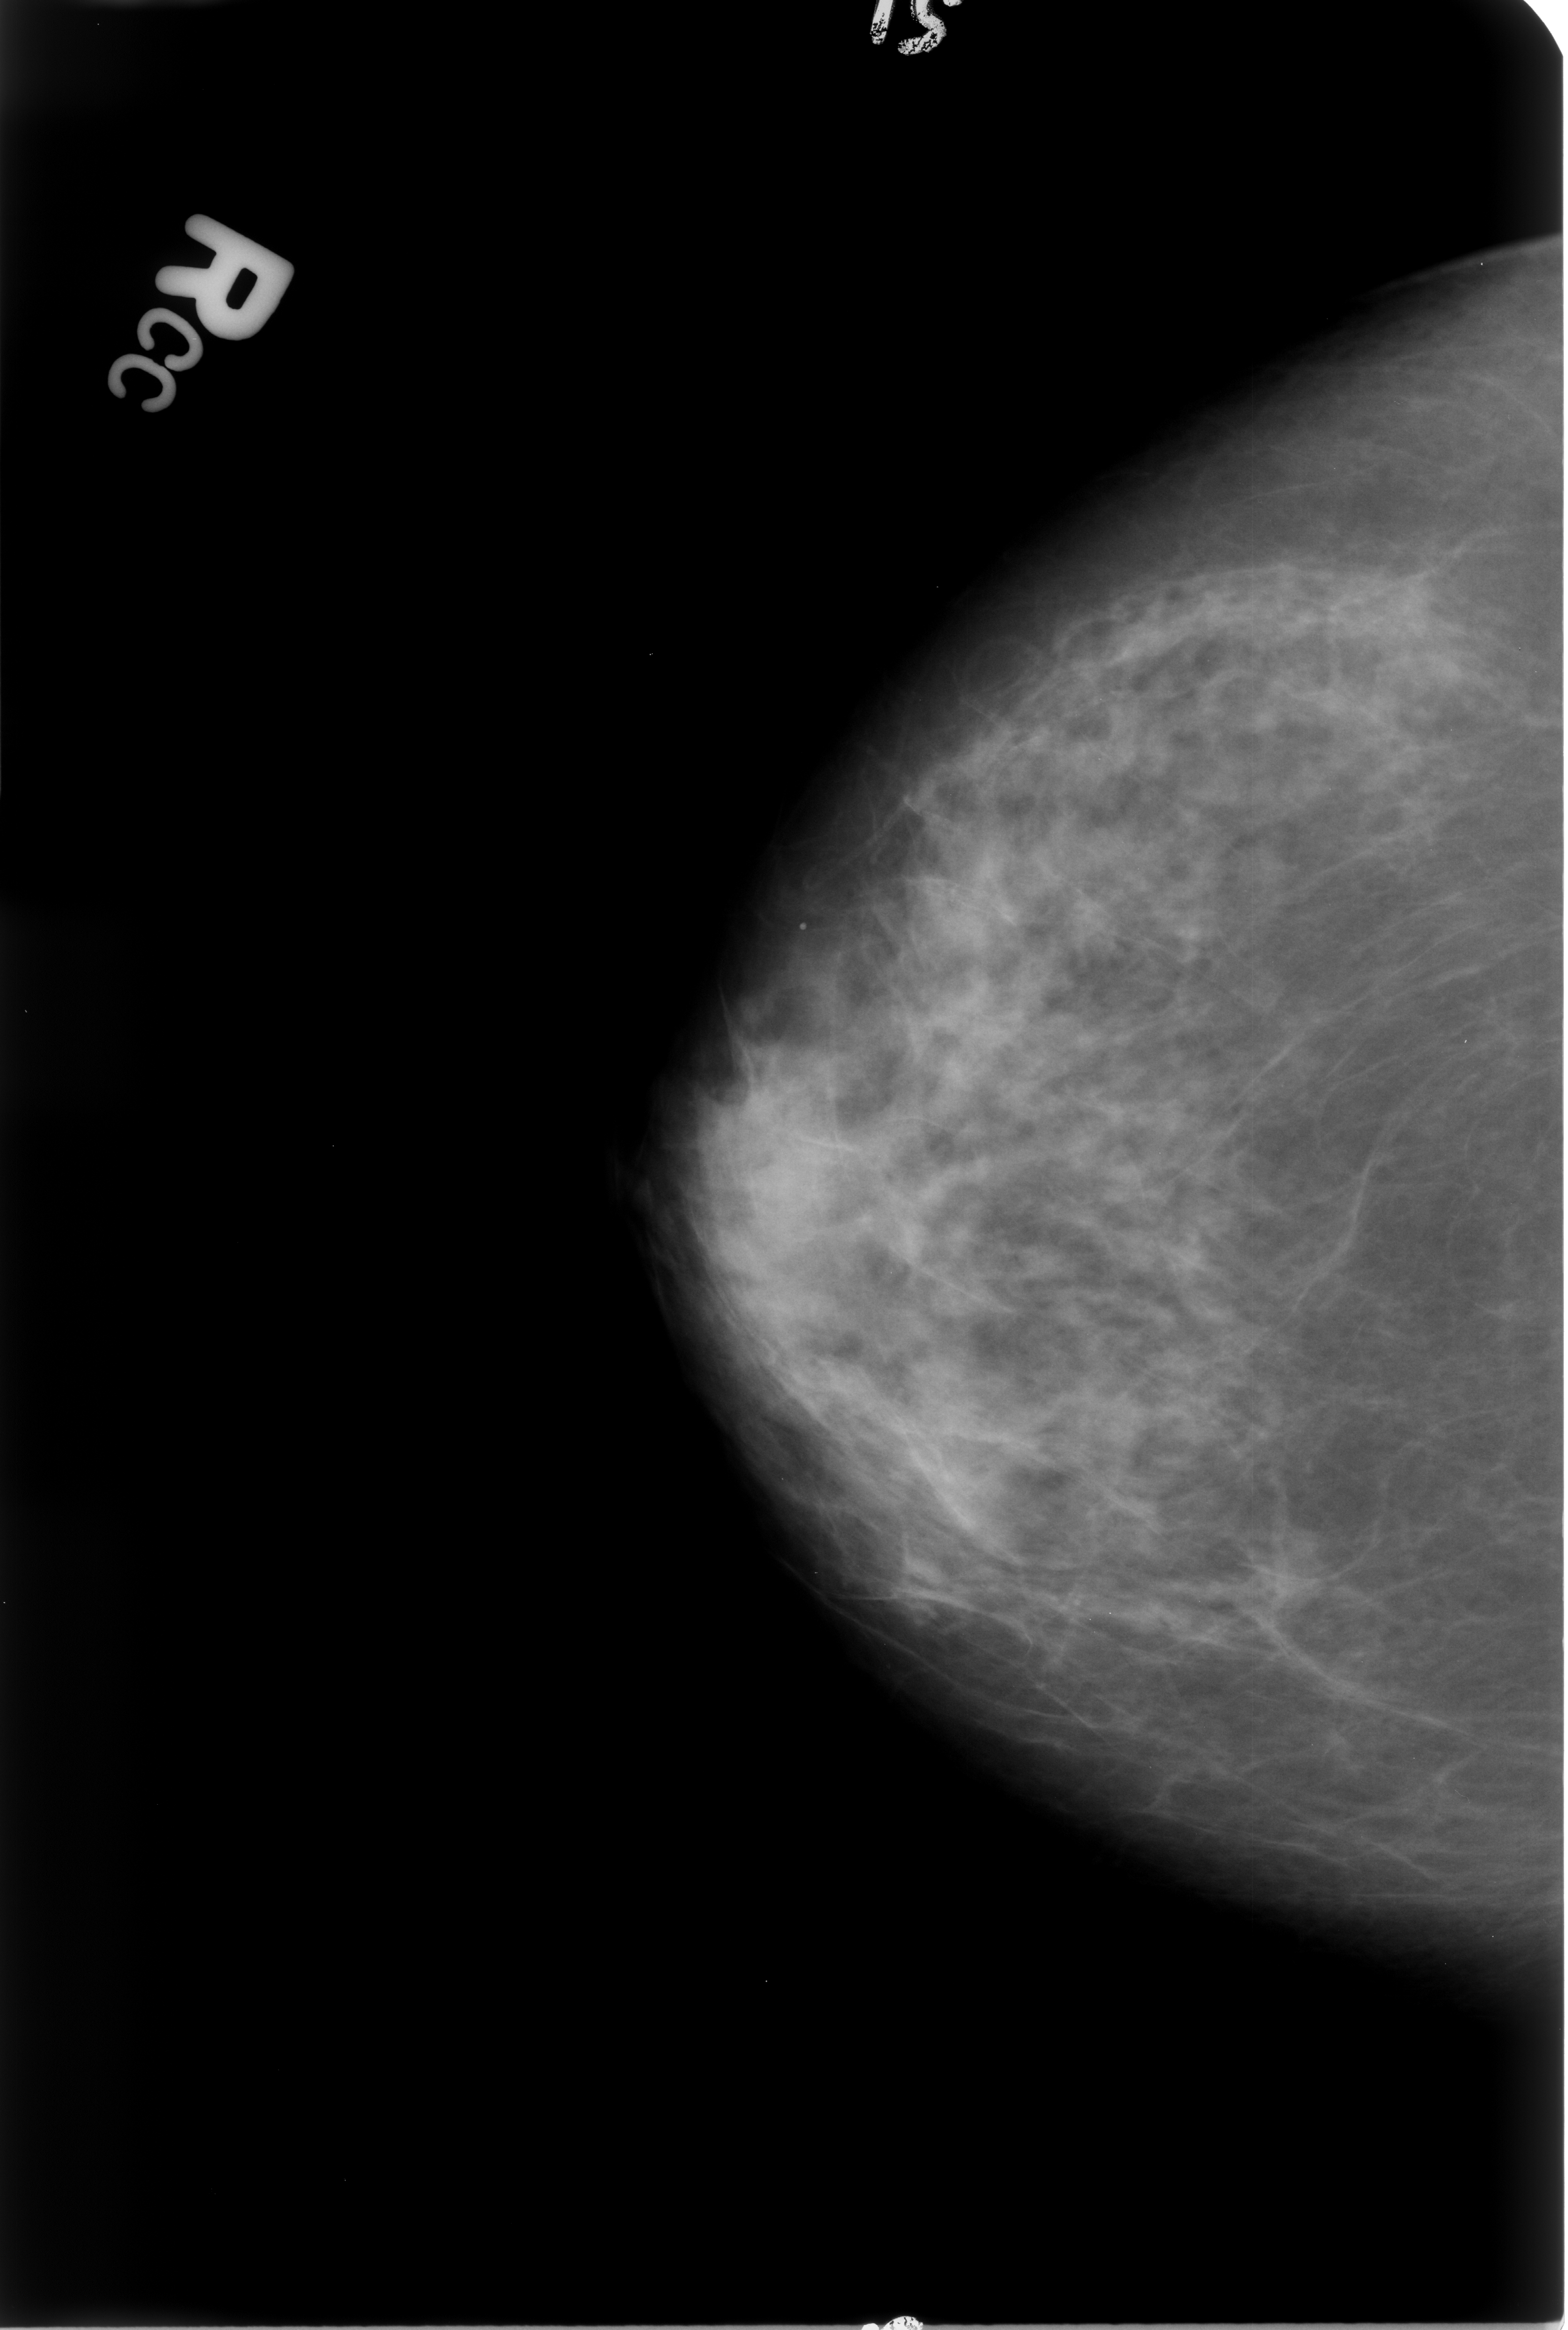
Mammogram (digitized film), right breast, craniocaudal (CC) view, breast composition: heterogeneously dense (BI-RADS density category 3 of 4).
- Marked findings (only marked abnormalities are described; nothing is implied about the rest of the image): Finding 1 of 2: calcifications, morphology punctate; BI-RADS assessment category 2; benign; no additional work-up was recommended (benign without callback).
- Finding 2 of 2: calcifications, morphology vascular; BI-RADS assessment category 2; subtlety rating 3 on a 1 (subtle) to 5 (obvious) scale; benign; no additional work-up was recommended (benign without callback).